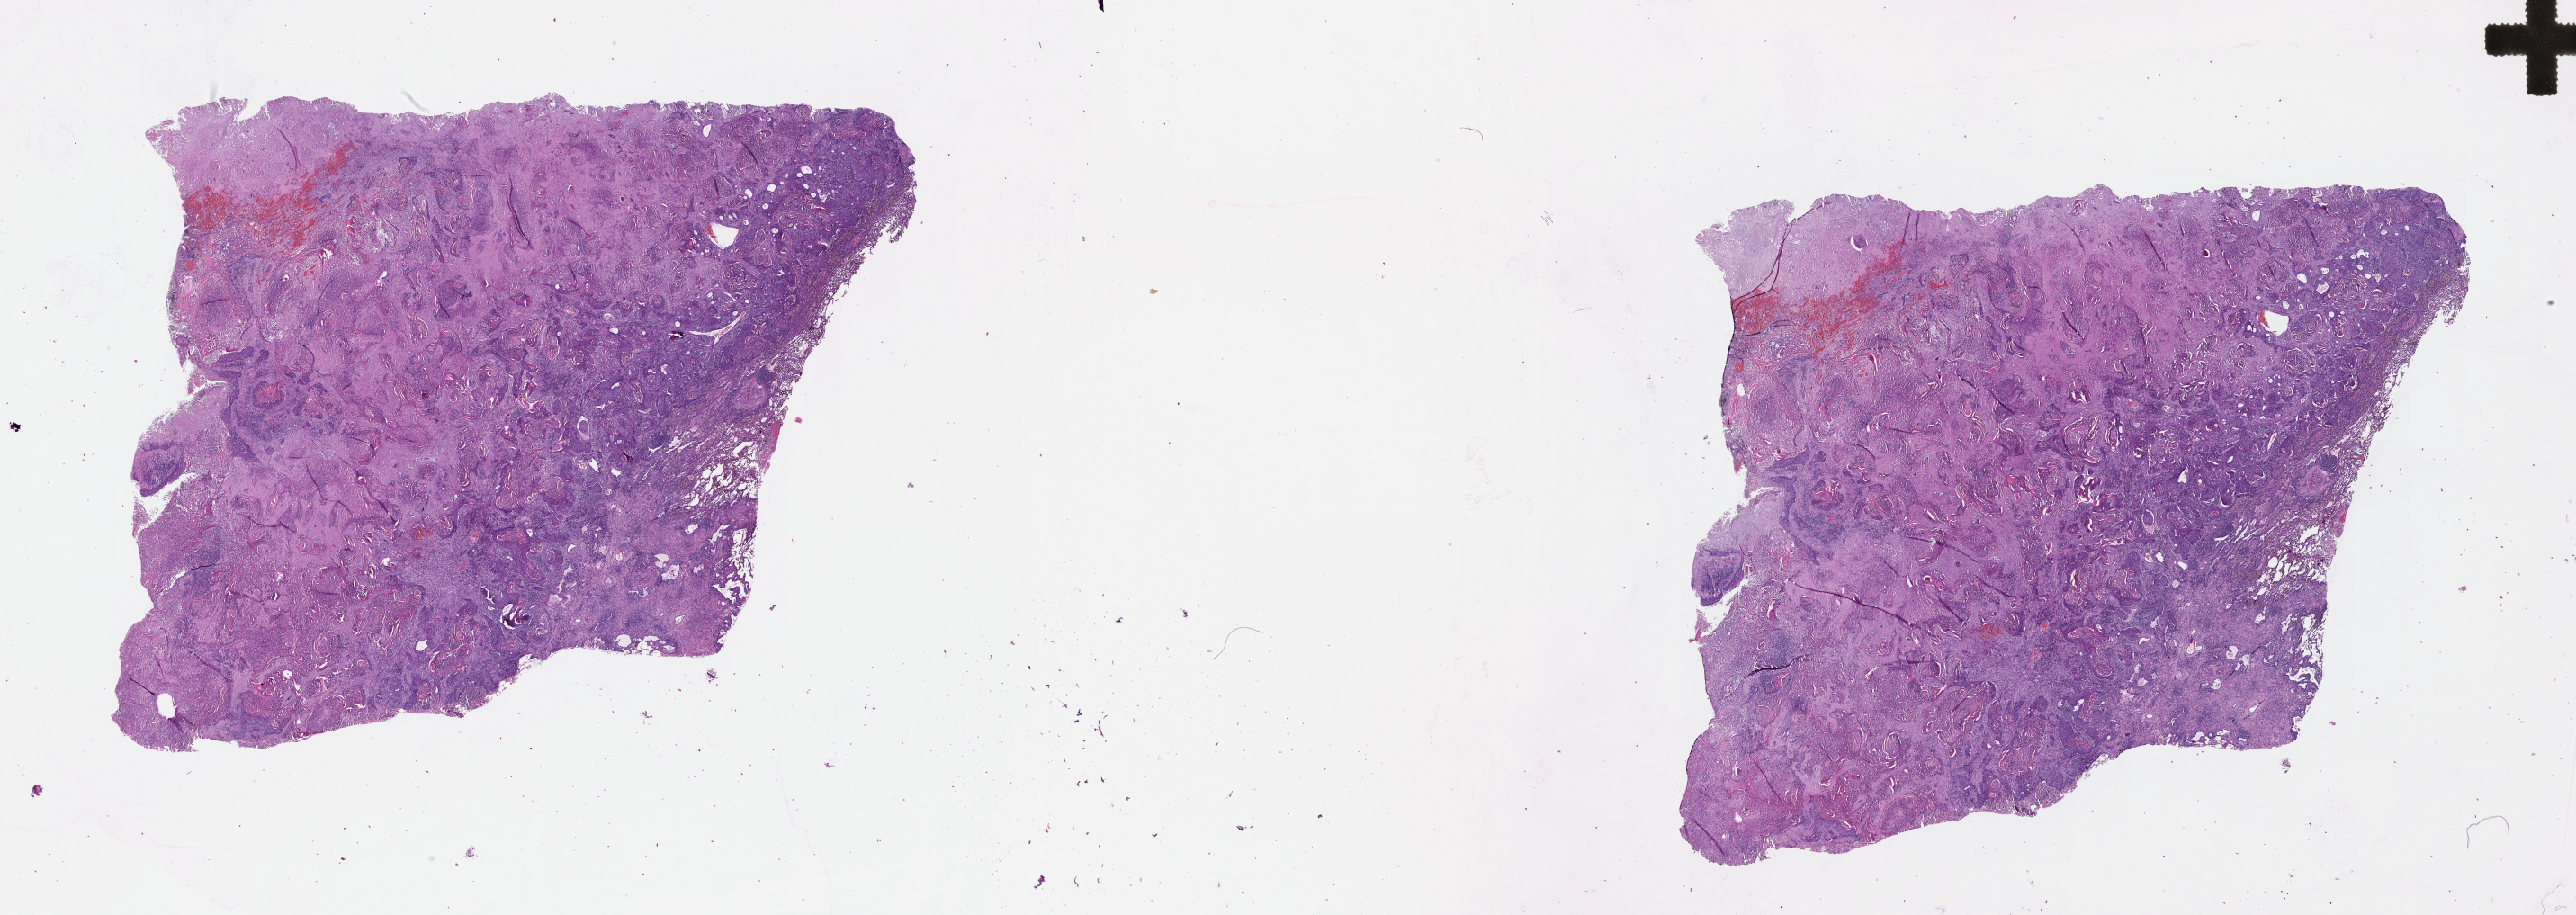
H&E-stained whole-slide image, a low-resolution overview of the entire scanned area, about 46.1 x 16.4 mm. Lung, tumour tissue. Patient: male, age 49 years.
Patient diagnosis (cohort enrolment): squamous cell carcinoma (lung).